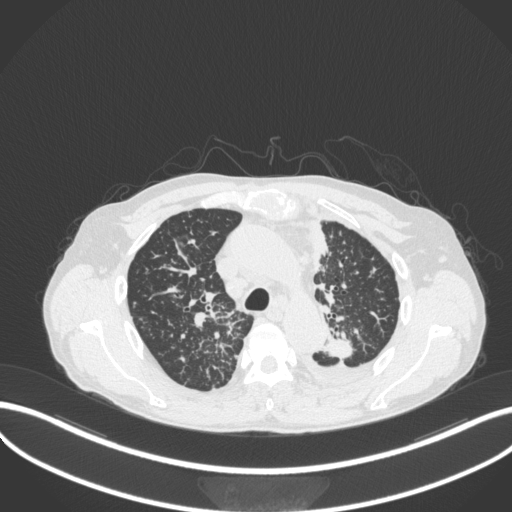
Chest CT, one axial slice; position 257 of 319 along the scan axis; reconstruction kernel B31f; 120 kVp; lung window (W 1500 / L -600 HU); 1 mm slice thickness; 512 × 512 image matrix, field of view 400 × 400 mm. Patient: male, 58 years. Case-level facts recorded for this patient, not image findings: clinical TNM (as recorded): T1c N3 M1.
Outlined on this slice (rectangle marked by the reading radiologist):
- lung tumour (recorded histology: adenocarcinoma): bounding box (x1, y1, x2, y2) in pixels: (321, 336, 358, 360)